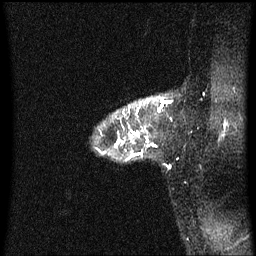
Breast MRI (dynamic contrast-enhanced), one sagittal slice. Slice 49 of 60 in the series (ordered by position). Dynamic contrast-enhanced series, image 2 of 3 at this slice position (ordered by acquisition). 1.5 T. TE 4.2 ms, TR 8.4 ms. 256 × 256 image matrix. Patient: female, 32 years.
Annotated regions visible in this slice (semi-automatically segmented with operator editing):
- analysis volume of interest (the breast-tissue region the enhancement analysis was run in; not a lesion): box from (x=106, y=98) to (x=163, y=159) px
- tumour enhancement mask (voxels above the 70 % enhancement threshold inside the analysis volume of interest): (x=116, y=110)–(x=139, y=149)